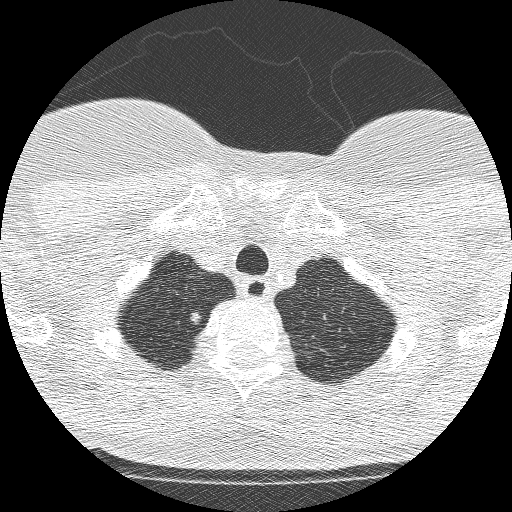
Low-dose screening chest CT, axial slice; second annual screen; lung window (W 1500 / L -600 HU); 1.25 mm slice thickness; 120 kVp; slice 218 of 250 in the series; 512 × 512 image matrix, field of view 257 × 257 mm. Female, age 61 years at enrolment.
• Expert-annotated lung lesion, bounding box [x1, y1, x2, y2] px = [160, 299, 214, 341].
• Screening reader's record for this exam (one nodule recorded; not confirmed to be the boxed lesion): non-calcified nodule or mass ≥4 mm, right upper lobe, 11 × 8 mm, poorly defined margins, mixed attenuation, pre-existing on the prior screen: yes; interval growth: yes.
• Official screen result: positive, change unspecified: nodule(s) >= 4 mm or enlarging nodule(s), mass(es), or other non-specific abnormalities suspicious for lung cancer.
• Lung cancer was diagnosed 28 days after this screen: adenocarcinoma, NOS, right upper lobe, poorly differentiated (G3), 12 mm at pathology.